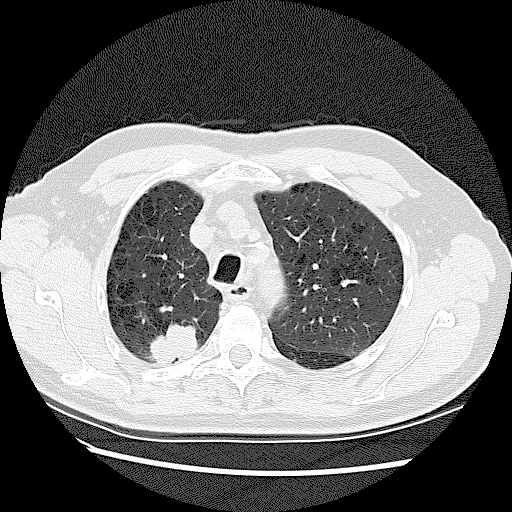
Chest CT (low-dose screening protocol), one axial image; first (baseline) screen; lung window (W 1500 / L -600 HU); 2.5 mm slice thickness. Male, age 72 years at enrolment. Current smoker at enrolment.
- Expert reader's lesion annotation, bounding box [x1, y1, x2, y2] px = [136, 308, 213, 375].
- The screening reader recorded 2 non-calcified nodules or masses ≥4 mm on this exam (right upper lobe, right upper lobe); which of them this box marks is not recorded.